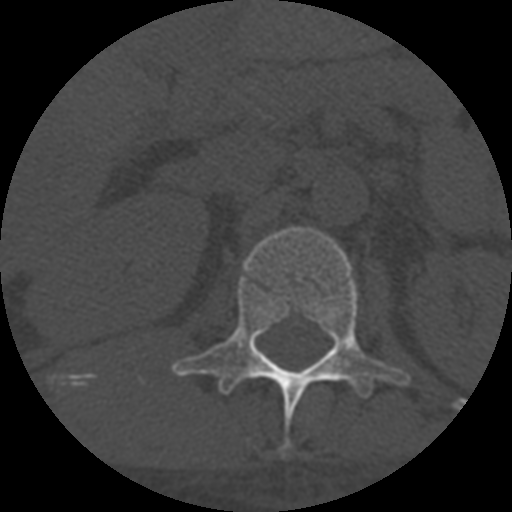
CT including the spine, one axial slice; position 288 of 708 along the scan axis; reconstruction kernel STANDARD; one of 3 acquisitions stored at this slice position; bone window (W 1800 / L 400 HU); 512 × 512 image matrix, field of view 160 × 160 mm. Patient age 55 years. Case-level facts recorded for this patient, not image findings: primary cancer: colon; vertebrae with lytic lesions (as recorded): T12, L1, L5.
Annotated regions visible in this slice (semi-automatically segmented with operator editing):
- L1 vertebra: bounding box (x1, y1, x2, y2) in pixels: (172, 227, 410, 454)